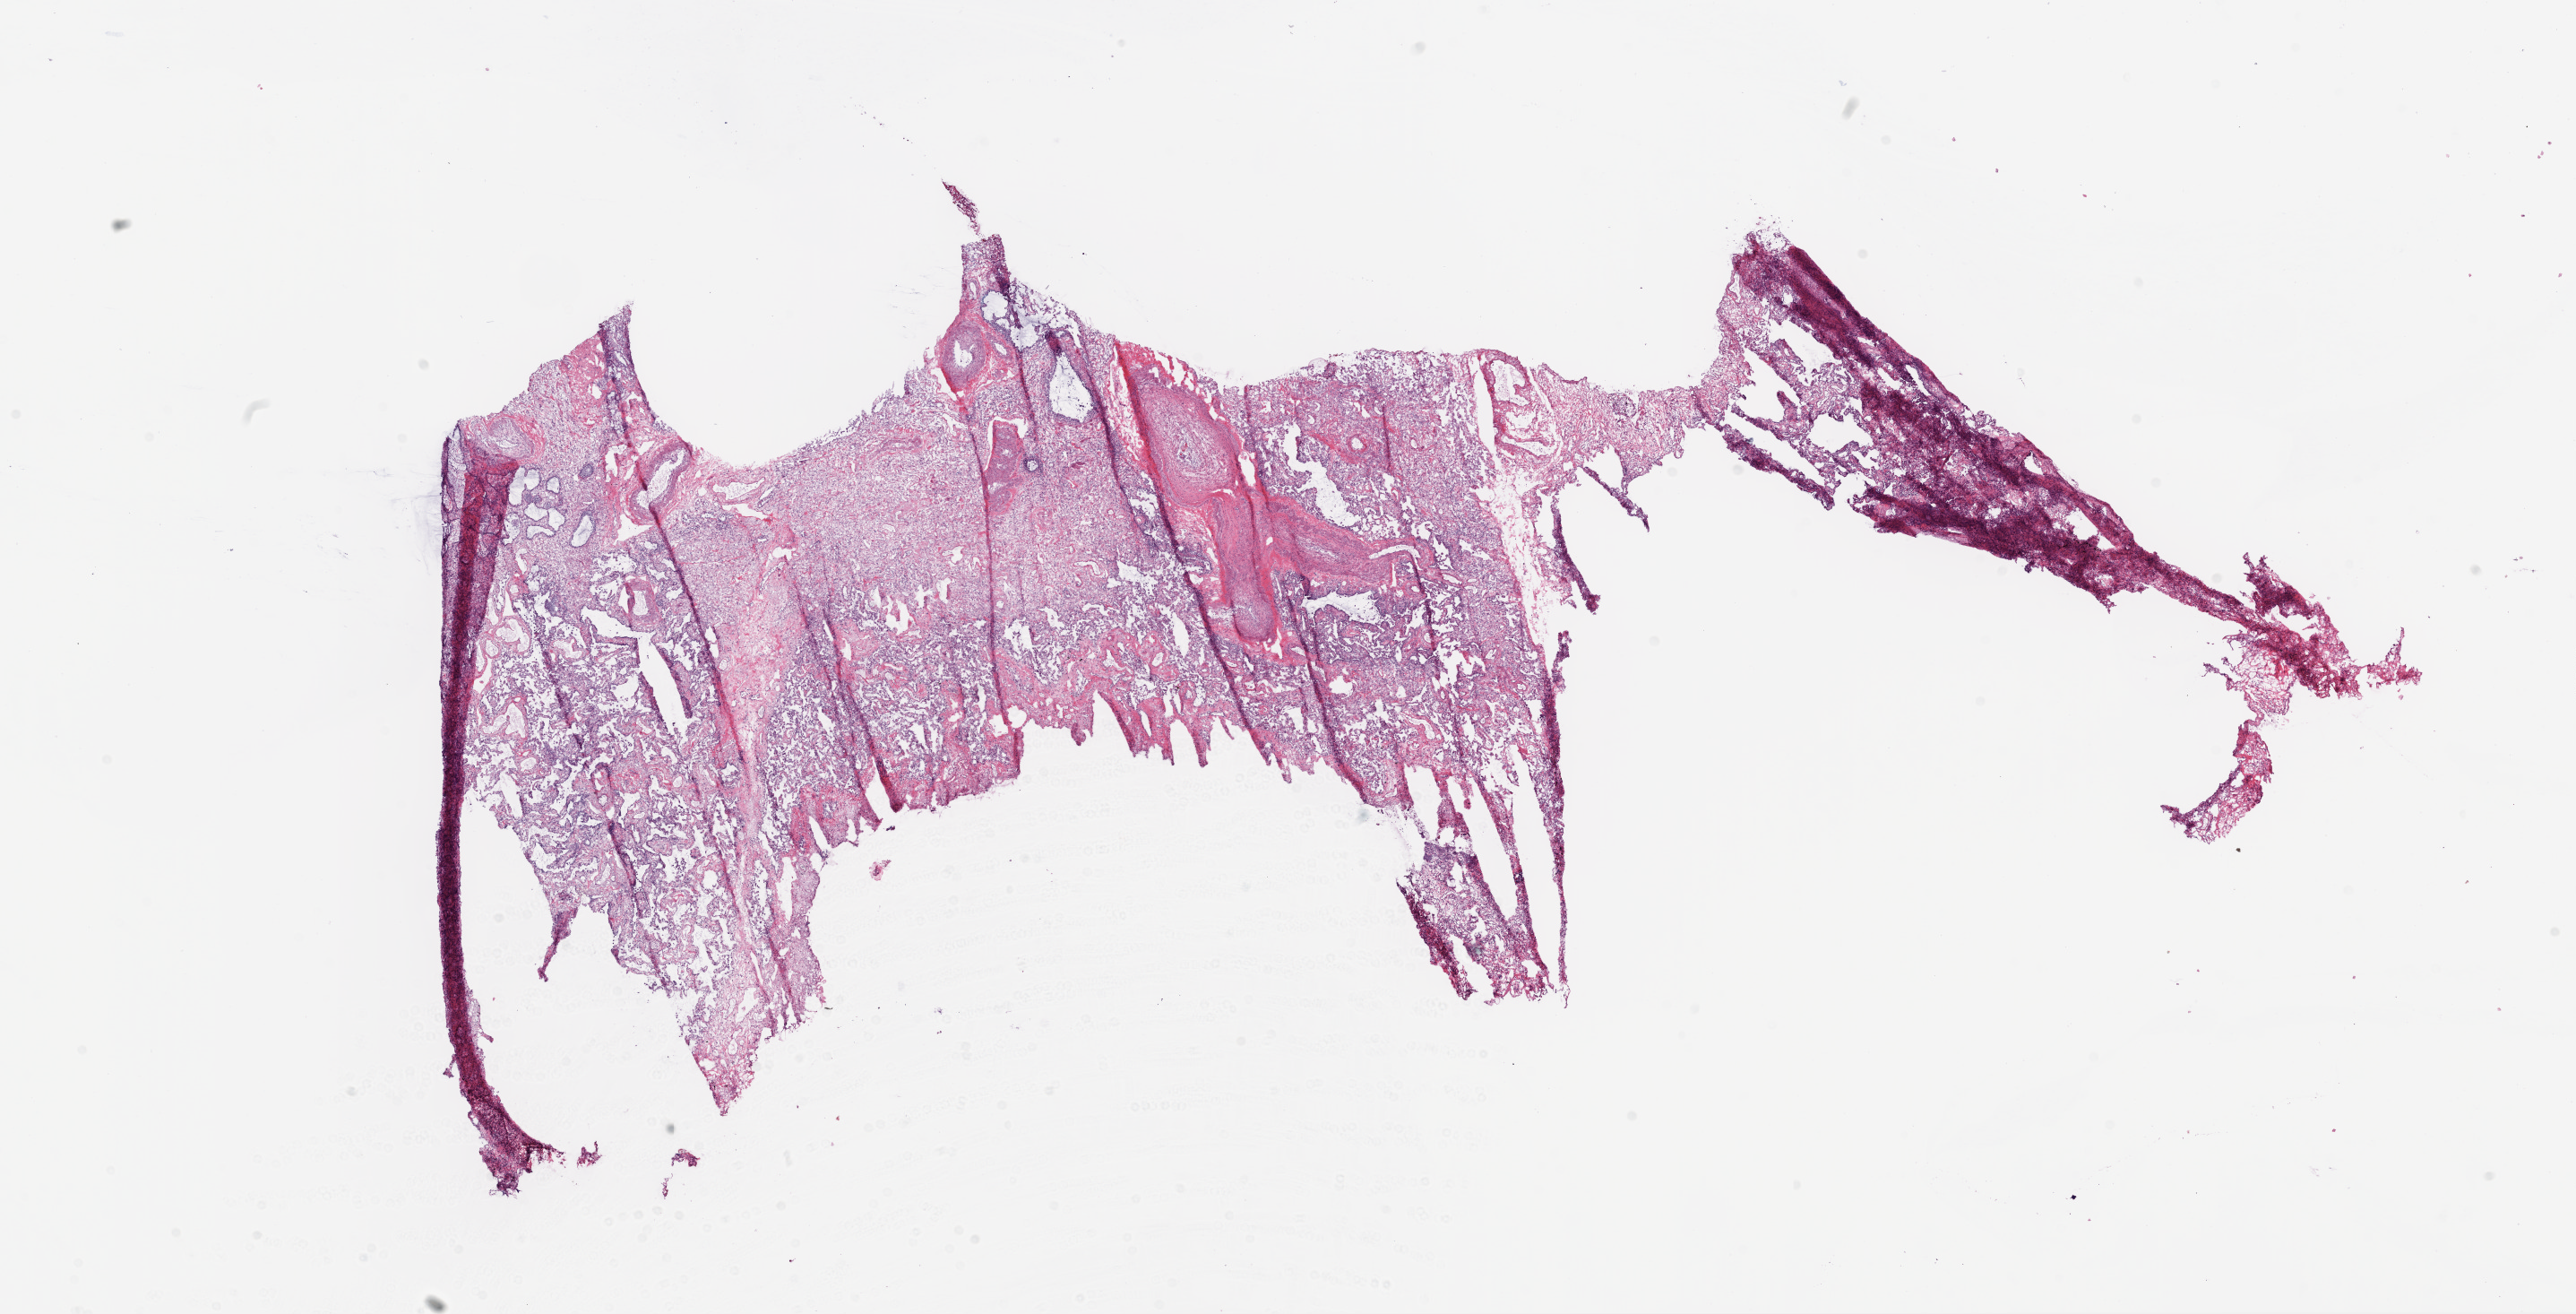
Digitized H&E tissue section (whole slide), shown as a low-resolution overview of the whole scanned area (about 23.1 x 11.8 mm), frozen section from the bottom of the tissue portion, sample: solid tissue normal (non-tumour tissue), lung. Female, age 74 years at initial diagnosis.
This section: solid tissue normal (non-tumour) sample from the same patient. Patient diagnosis: Basaloid squamous cell carcinoma (upper lobe, lung).